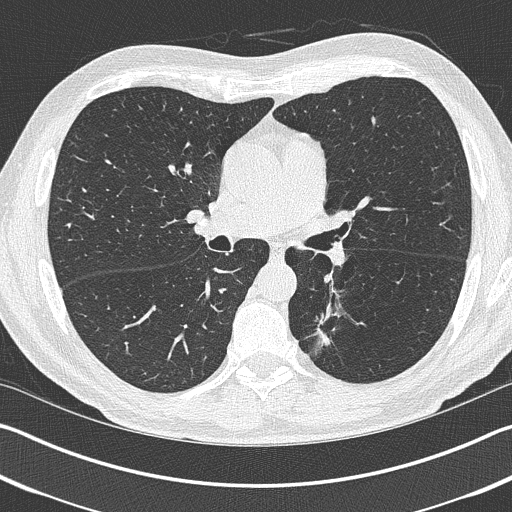
Low-dose screening chest CT, axial slice. Baseline annual screen. Lung window (W 1500 / L -600 HU). 1 mm slice thickness. 120 kVp. Slice 165 of 402 in the series. 512 × 512 image matrix, field of view 340 × 340 mm. Male, age 69 years at enrolment. Current smoker at enrolment.
- Expert reader's lesion annotation, box from (x=298, y=307) to (x=353, y=361) px.
- Screening reader's record for this exam (one nodule recorded; not confirmed to be the boxed lesion): non-calcified nodule or mass ≥4 mm, left upper lobe, 19 × 19 mm, spiculated (stellate) margins, pre-existing on the prior screen: yes.
- Official screen result: positive, change unspecified: nodule(s) >= 4 mm or enlarging nodule(s), mass(es), or other non-specific abnormalities suspicious for lung cancer.
- Participant outcome: lung cancer diagnosed 202 days after this screen — non-small cell carcinoma, left lower lobe, stage IIIA (AJCC 6th edition), 20 mm at pathology.